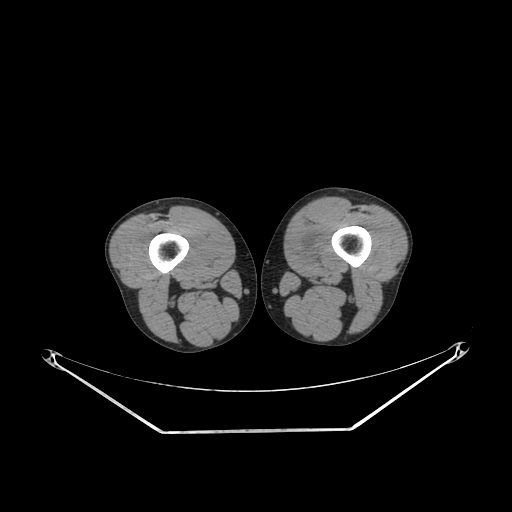
CT of an extremity soft-tissue mass (from a PET/CT study), one axial slice; slice 228 of 311 in the series (ordered by position); soft-tissue window (W 400 / L 40 HU); 3.75 mm slice thickness; 512 × 512 image matrix, field of view 500 × 500 mm. Male patient. Case-level facts recorded for this patient, not image findings: histological type: mixoid liposarcoma; grade: low; site of the primary tumour: left thigh.
Annotated regions visible in this slice (expert contour drawn on MRI and transferred to this co-registered scan by the dataset authors):
- gross tumour volume (mass): bounding box (x1, y1, x2, y2) in pixels: (299, 238, 318, 257)